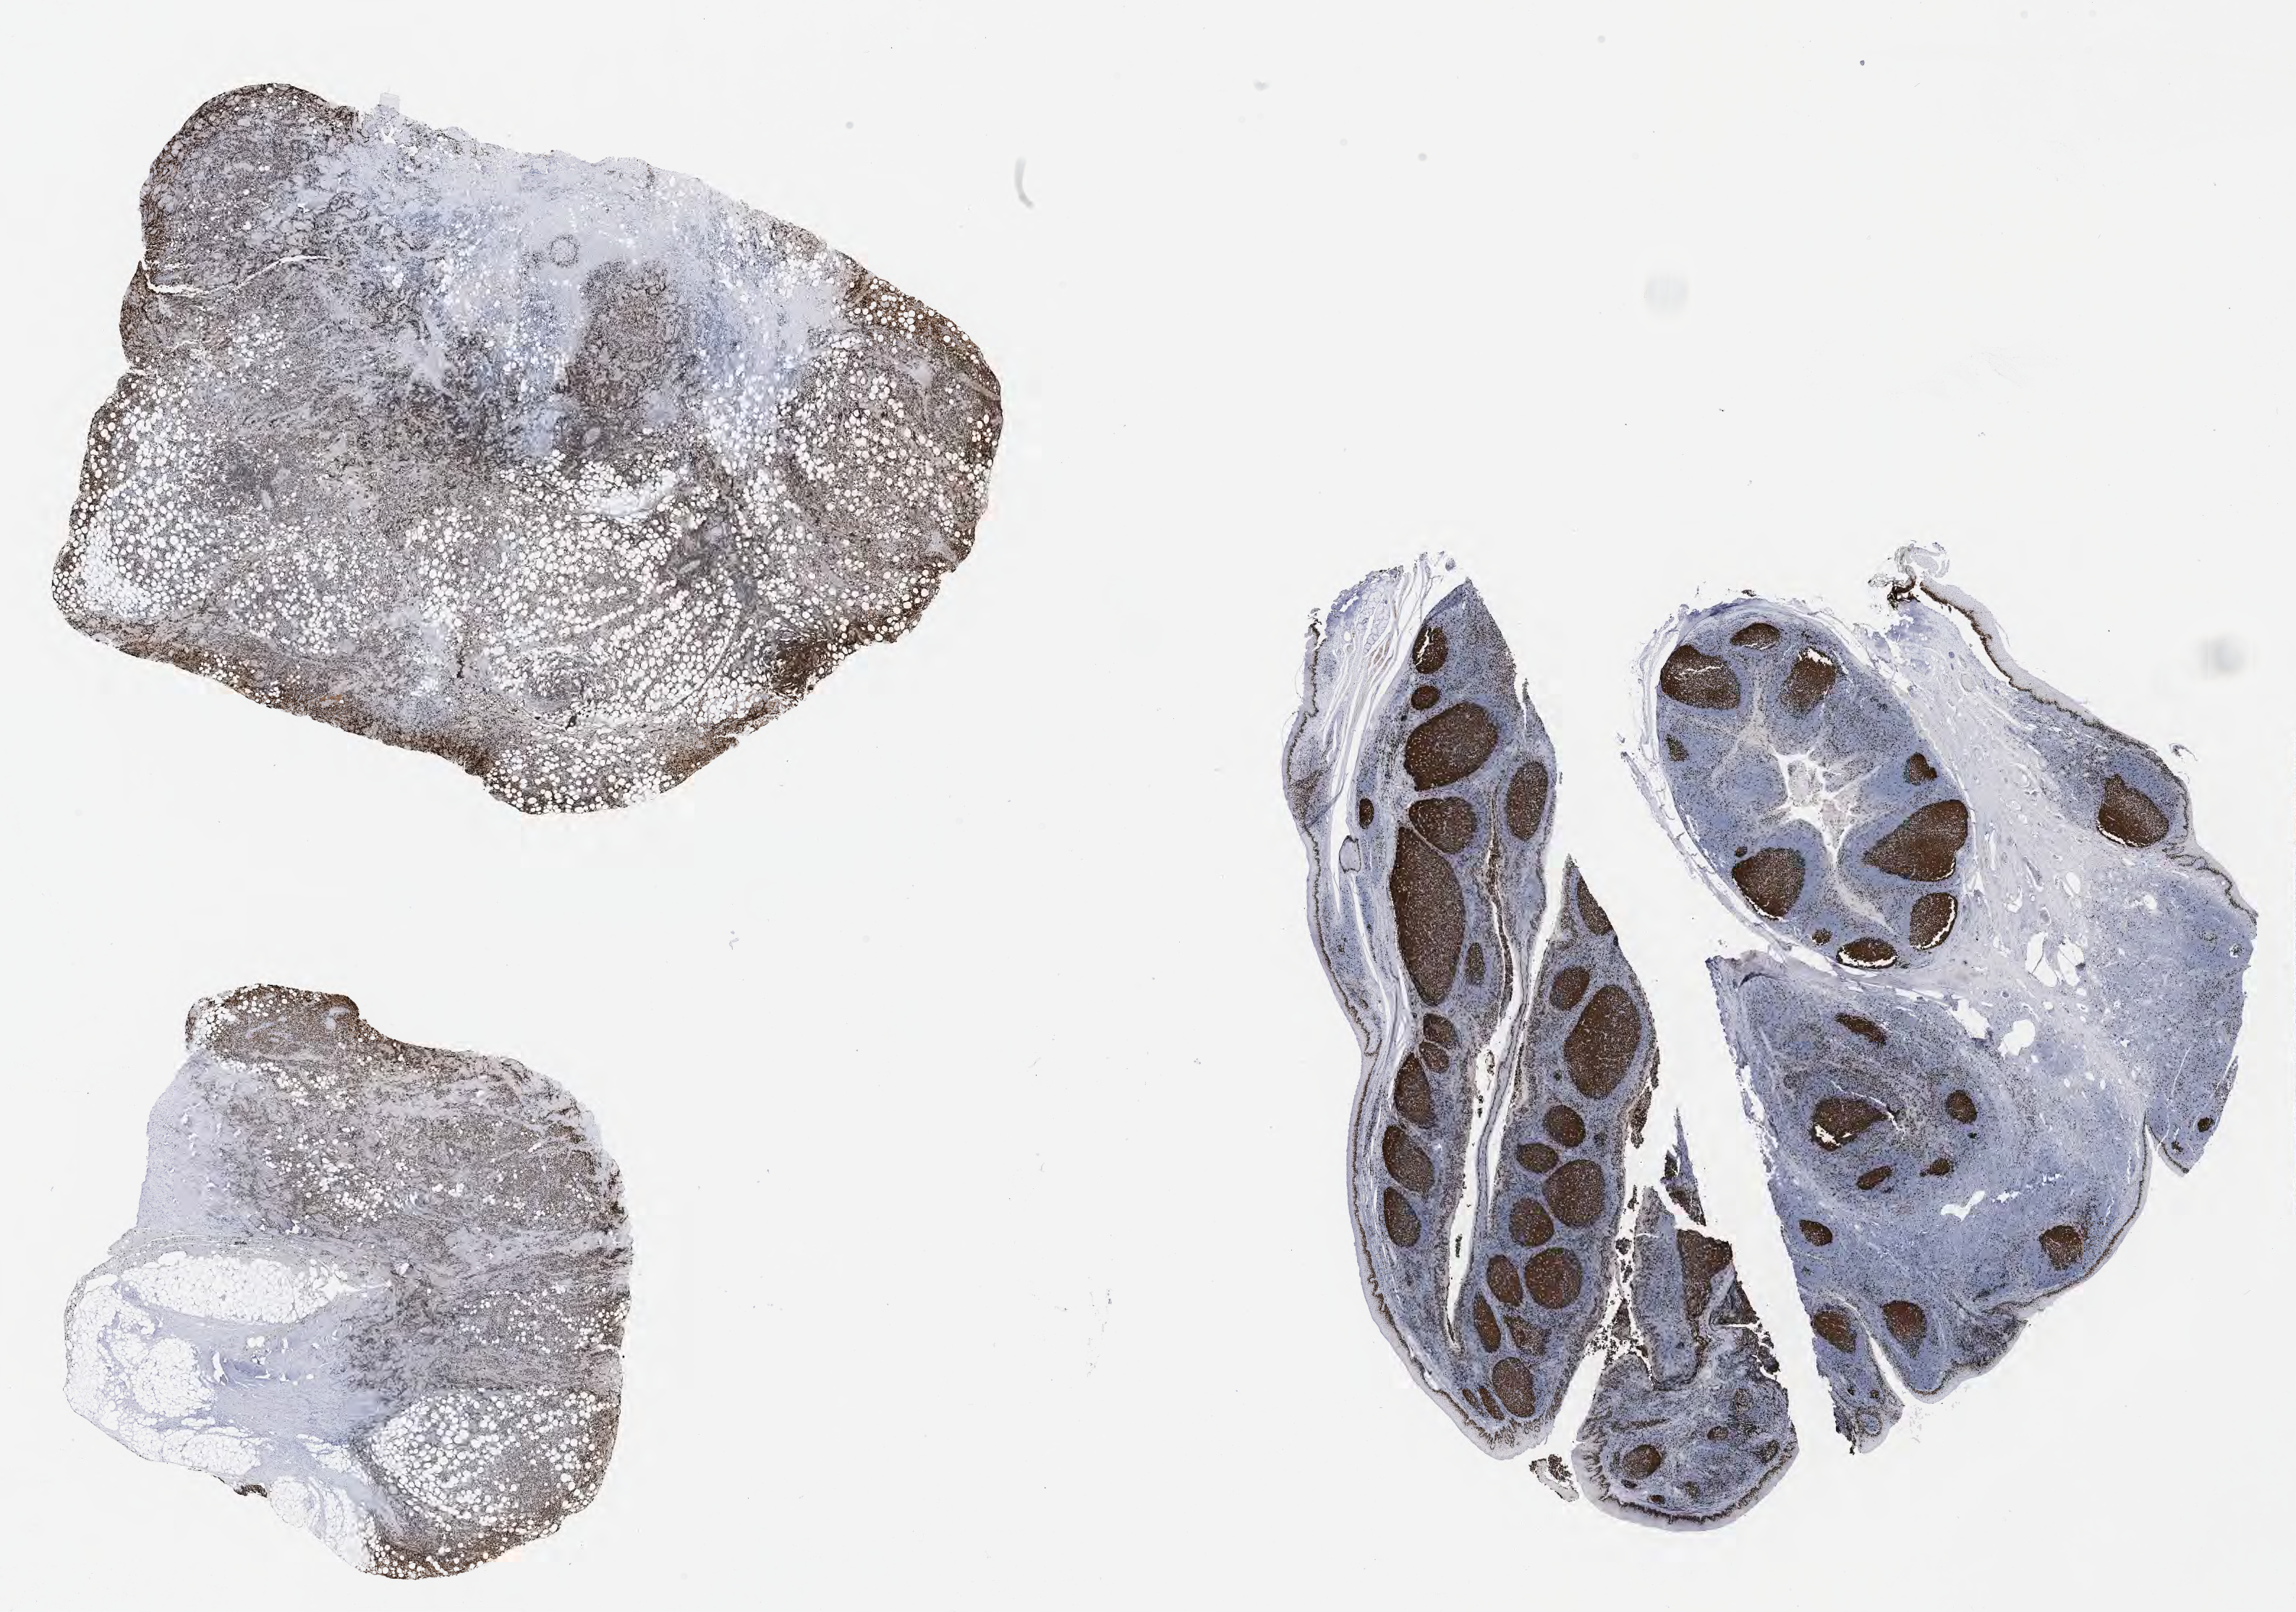
Whole-slide image, immunohistochemical stain for Ki-67 — whole scanned area (about 25.7 x 18.0 mm) shown as a low-resolution overview; tumor tissue; site: kidney. Patient male; aged 63.
Diagnosis: Diffuse large B-cell lymphoma, NOS.